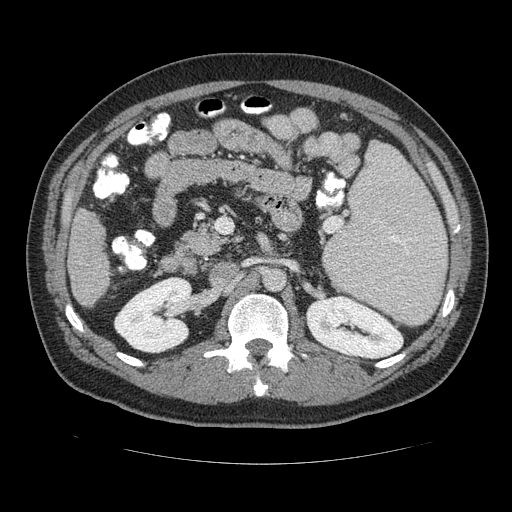
Contrast-enhanced abdominal CT (liver protocol), one axial slice. Position 55 of 113 along the scan axis. Reconstruction kernel STANDARD. Soft-tissue window (W 400 / L 40 HU). 2.5 mm slice thickness. 512 × 512 image matrix, field of view 400 × 400 mm. From the clinical record (not read from this slice): diagnosis: hepatocellular carcinoma (patient treated with transarterial chemoembolisation; whether this scan precedes or follows treatment is not stated here); TNM stage (as recorded): Stage-II; Child-Pugh class: B; tumour differentiation: moderately differentiated.
Annotated regions visible in this slice (semi-automatically segmented with operator editing):
- liver parenchyma outside the tumour (the mass and vessels are separate outlines, so this box may not span the whole liver): box from (x=66, y=206) to (x=110, y=310) px